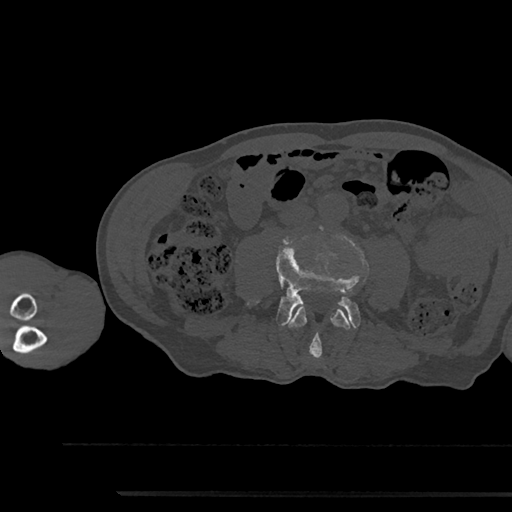
CT including the spine, one axial slice. Position 442 of 797 along the scan axis. Reconstruction kernel Br40s/3. 120 kVp. Bone window (W 1800 / L 400 HU). 512 × 512 image matrix, field of view 367 × 367 mm. Patient: male, 79 years. From the clinical record (not read from this slice): primary cancer: prostate.
Outlined on this slice (semi-automatic segmentation, software-assisted and operator-edited):
- L3 vertebra: bounding box <288,304,351,358> (left, top, right, bottom; pixels)
- L4 vertebra: <248,238,360,328>